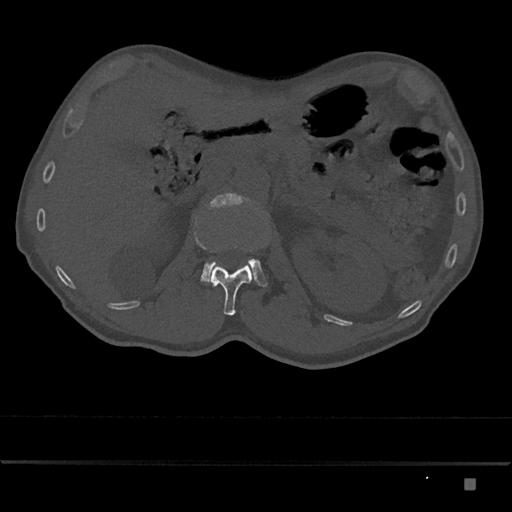
CT including the spine, one axial slice; position 521 of 797 along the scan axis; bone window (W 1800 / L 400 HU); 0.5 mm slice thickness; 512 × 512 image matrix. Patient: male, 72 years. From the clinical record (not read from this slice): primary cancer: prostate.
Structures marked on this image (semi-automatically segmented with operator editing):
- L1 vertebra: bounding box <208,263,253,316> (left, top, right, bottom; pixels)
- L2 vertebra: <201,193,267,287>